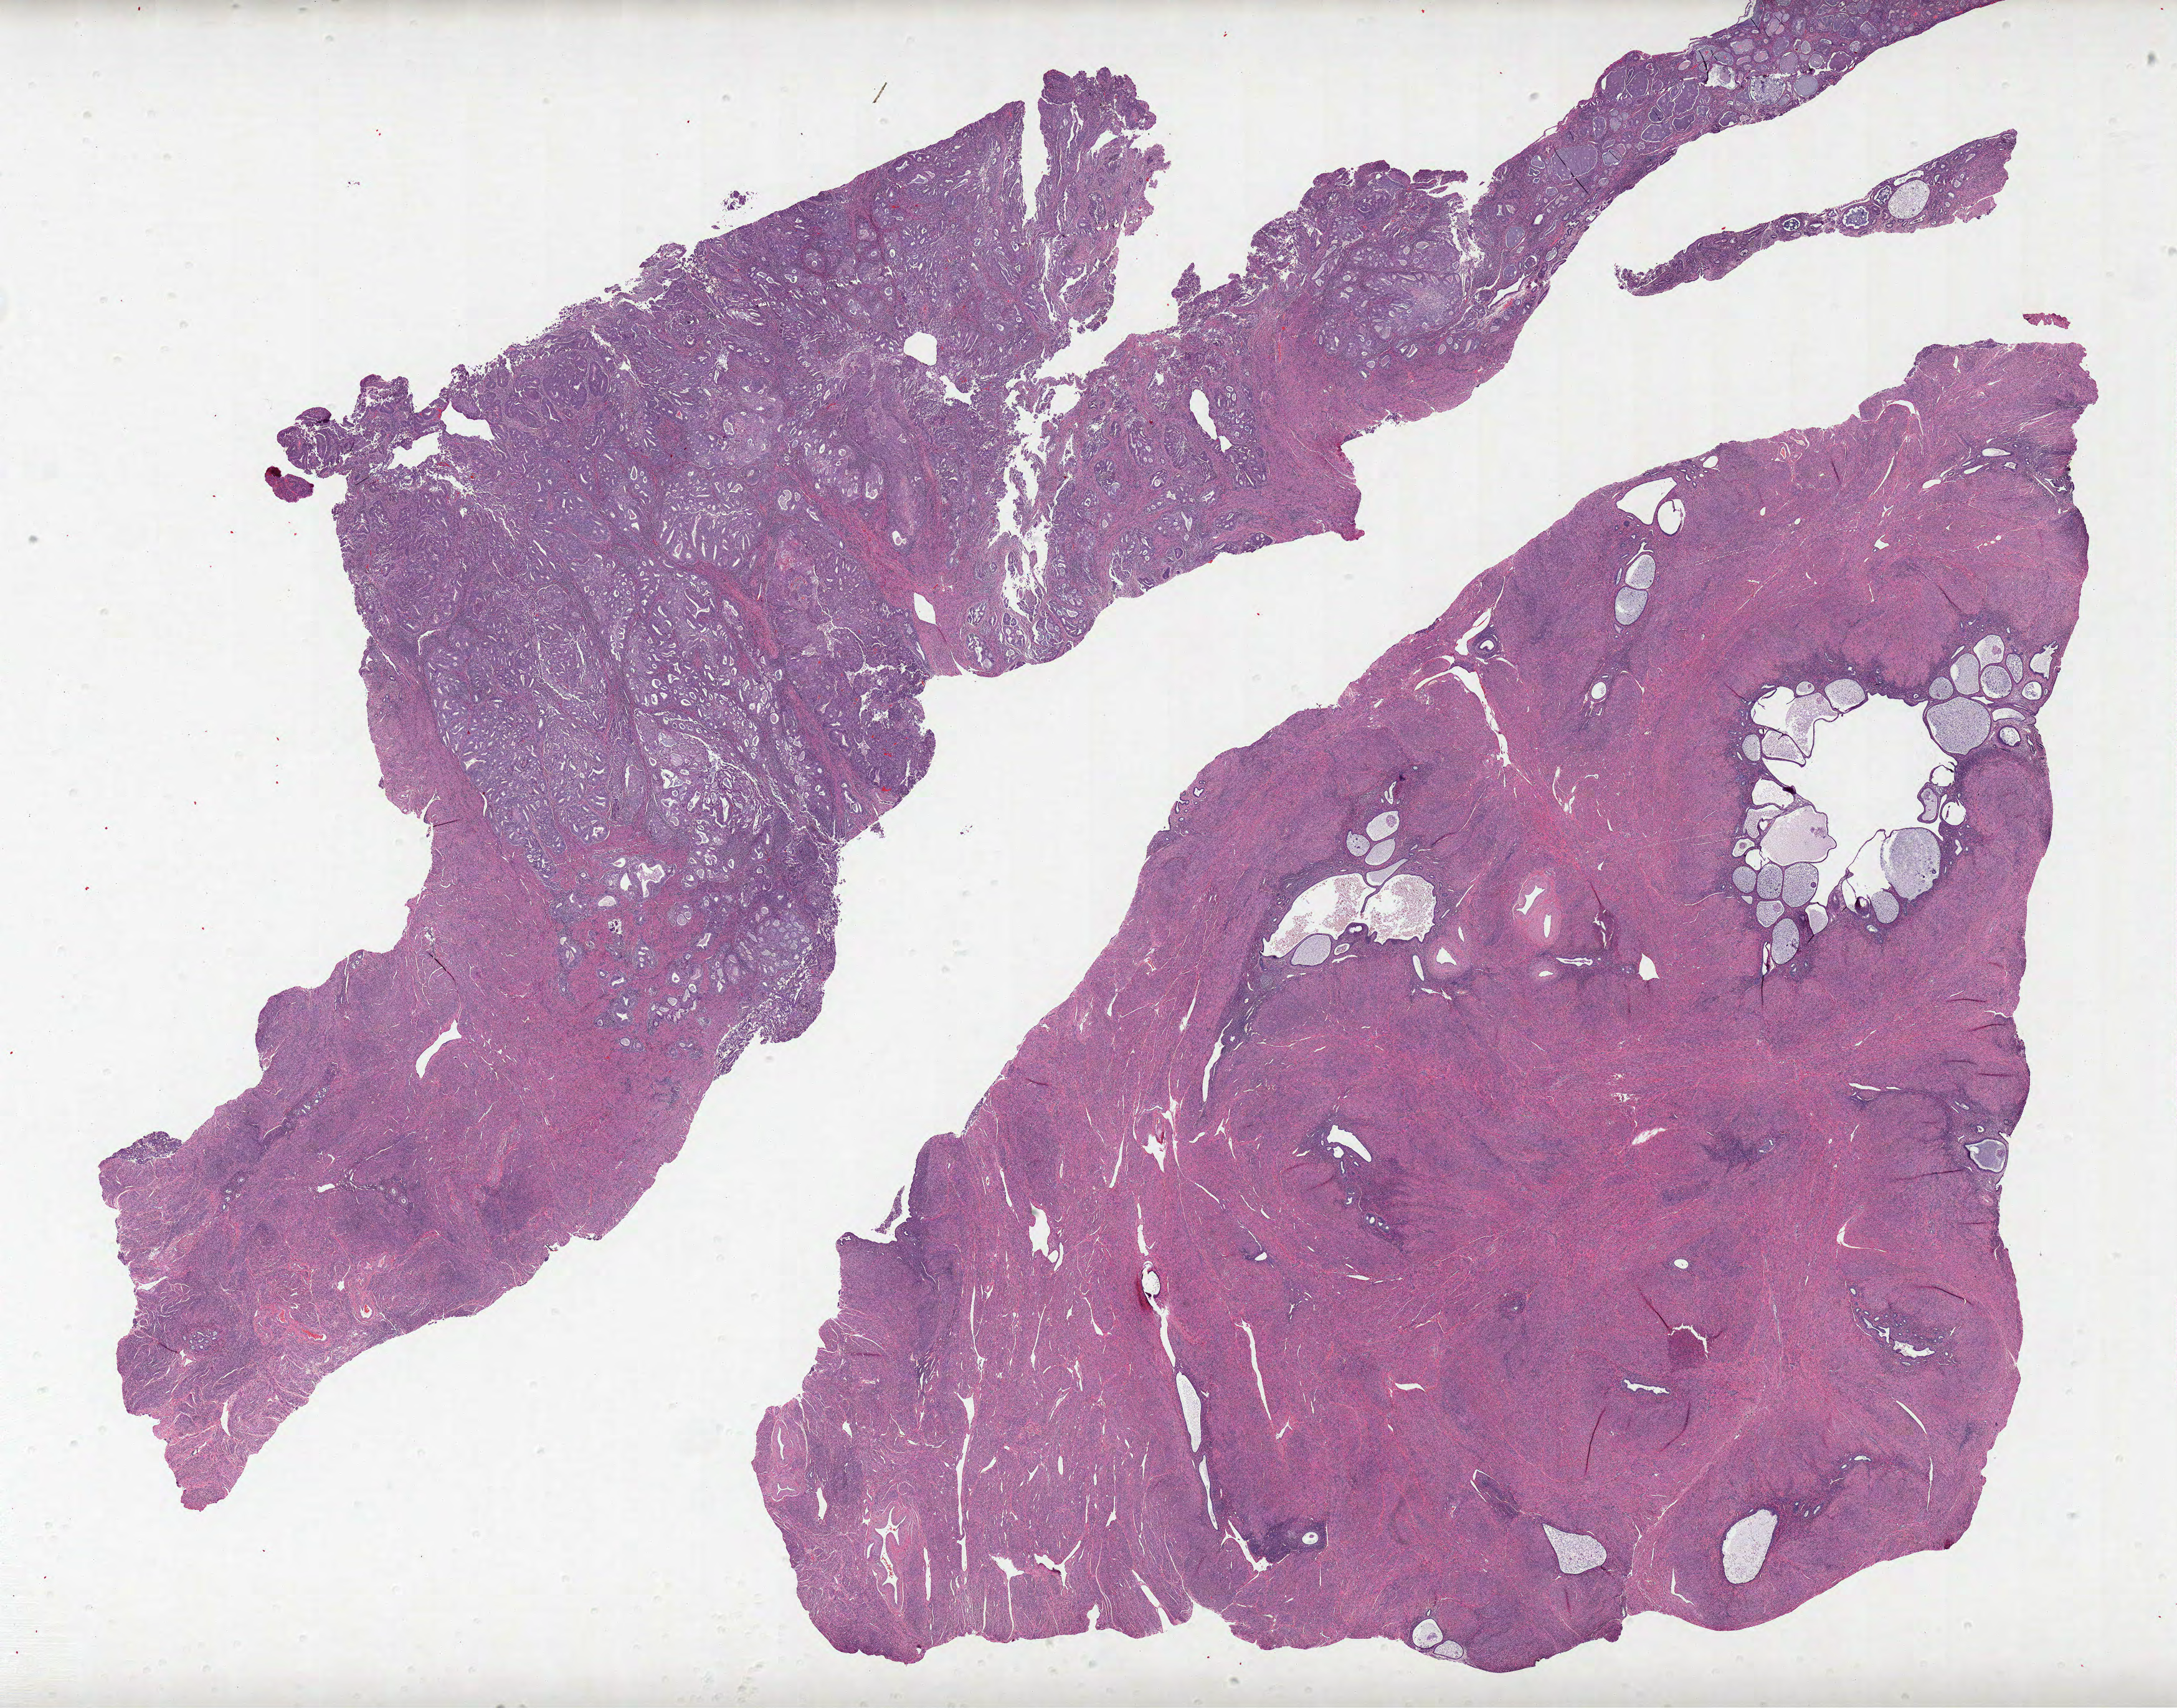
Digitized Hematoxylin and eosin (H&E) stained tissue section (whole slide) — whole scanned area (about 27.8 x 21.8 mm, slide scanned at 20x) shown as a low-resolution overview; FFPE section; uterus, primary tumour sample. Patient: female, age at initial diagnosis 74 years. Histologic grade: G2 (moderately differentiated).
FIGO stage: IA. Pathologic diagnosis: Endometrioid adenocarcinoma, NOS. Lymph nodes positive (case pathology): 0 of 2 examined.